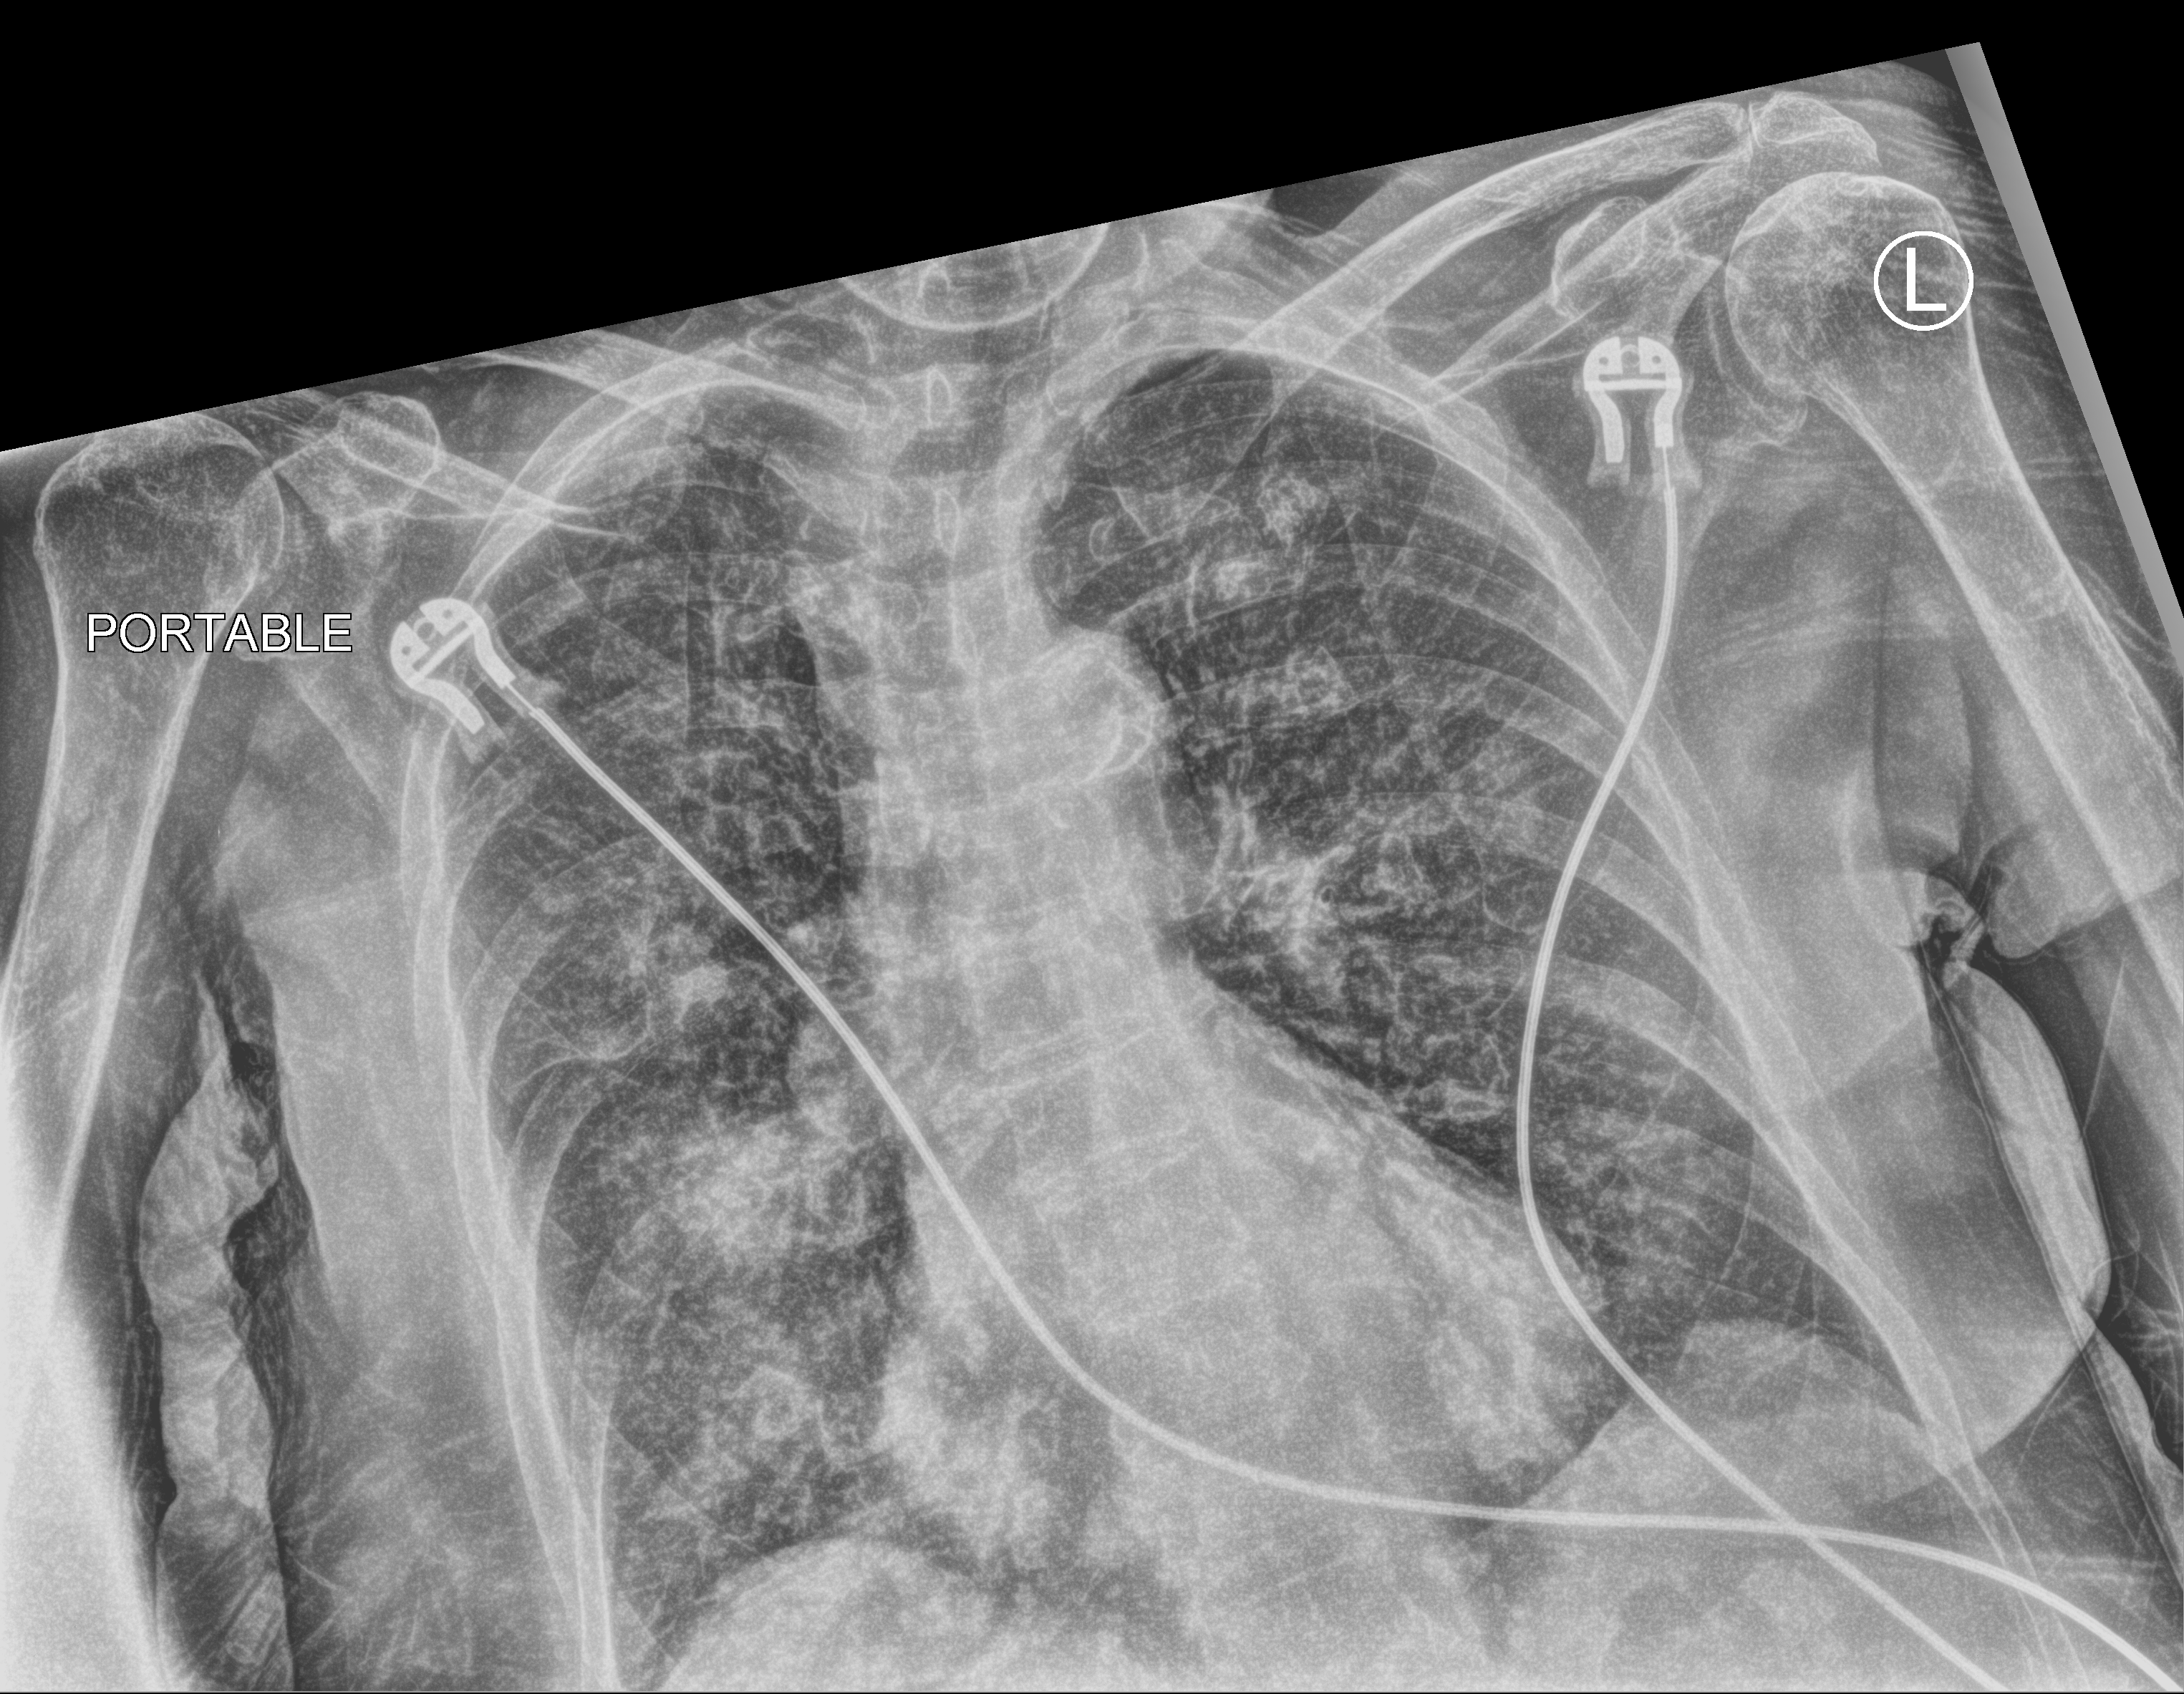
Bedside chest radiograph (computed radiography); anteroposterior (AP) projection. Female patient hospitalised with COVID-19, age 75–90 years.
Admission-level facts for this patient (not findings on this image; timing relative to this image not recorded): mechanically ventilated during this hospital stay: no; admitted to intensive care during this hospital stay: no; length of hospital stay: 2 days.